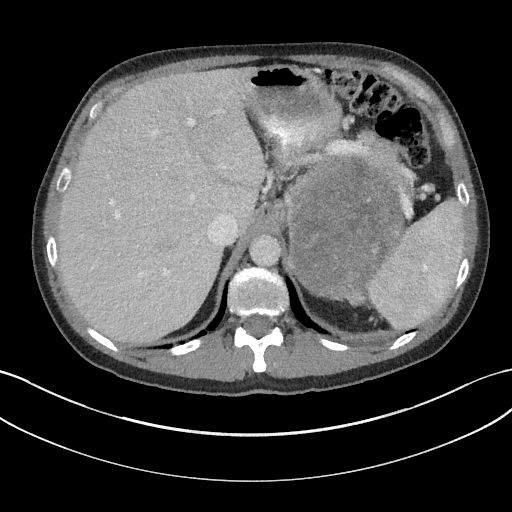
Contrast-enhanced abdominal CT, one axial slice; slice 124 of 147 in the series (ordered by position); reconstruction kernel I31f/3; intravenous contrast given; soft-tissue window (W 400 / L 40 HU); 3 mm slice thickness; 512 × 512 image matrix, field of view 384 × 384 mm. Patient: male, 58 years. From the clinical record (not read from this slice): diagnosis: adrenocortical carcinoma; tumour side: left adrenal; tumour size at pathology: 22 cm; Ki-67 index: 26 %; stage (as recorded): 2.
Structures marked on this image (semi-automatically segmented with operator editing):
- mass: bounding box <289,159,399,297> (left, top, right, bottom; pixels)